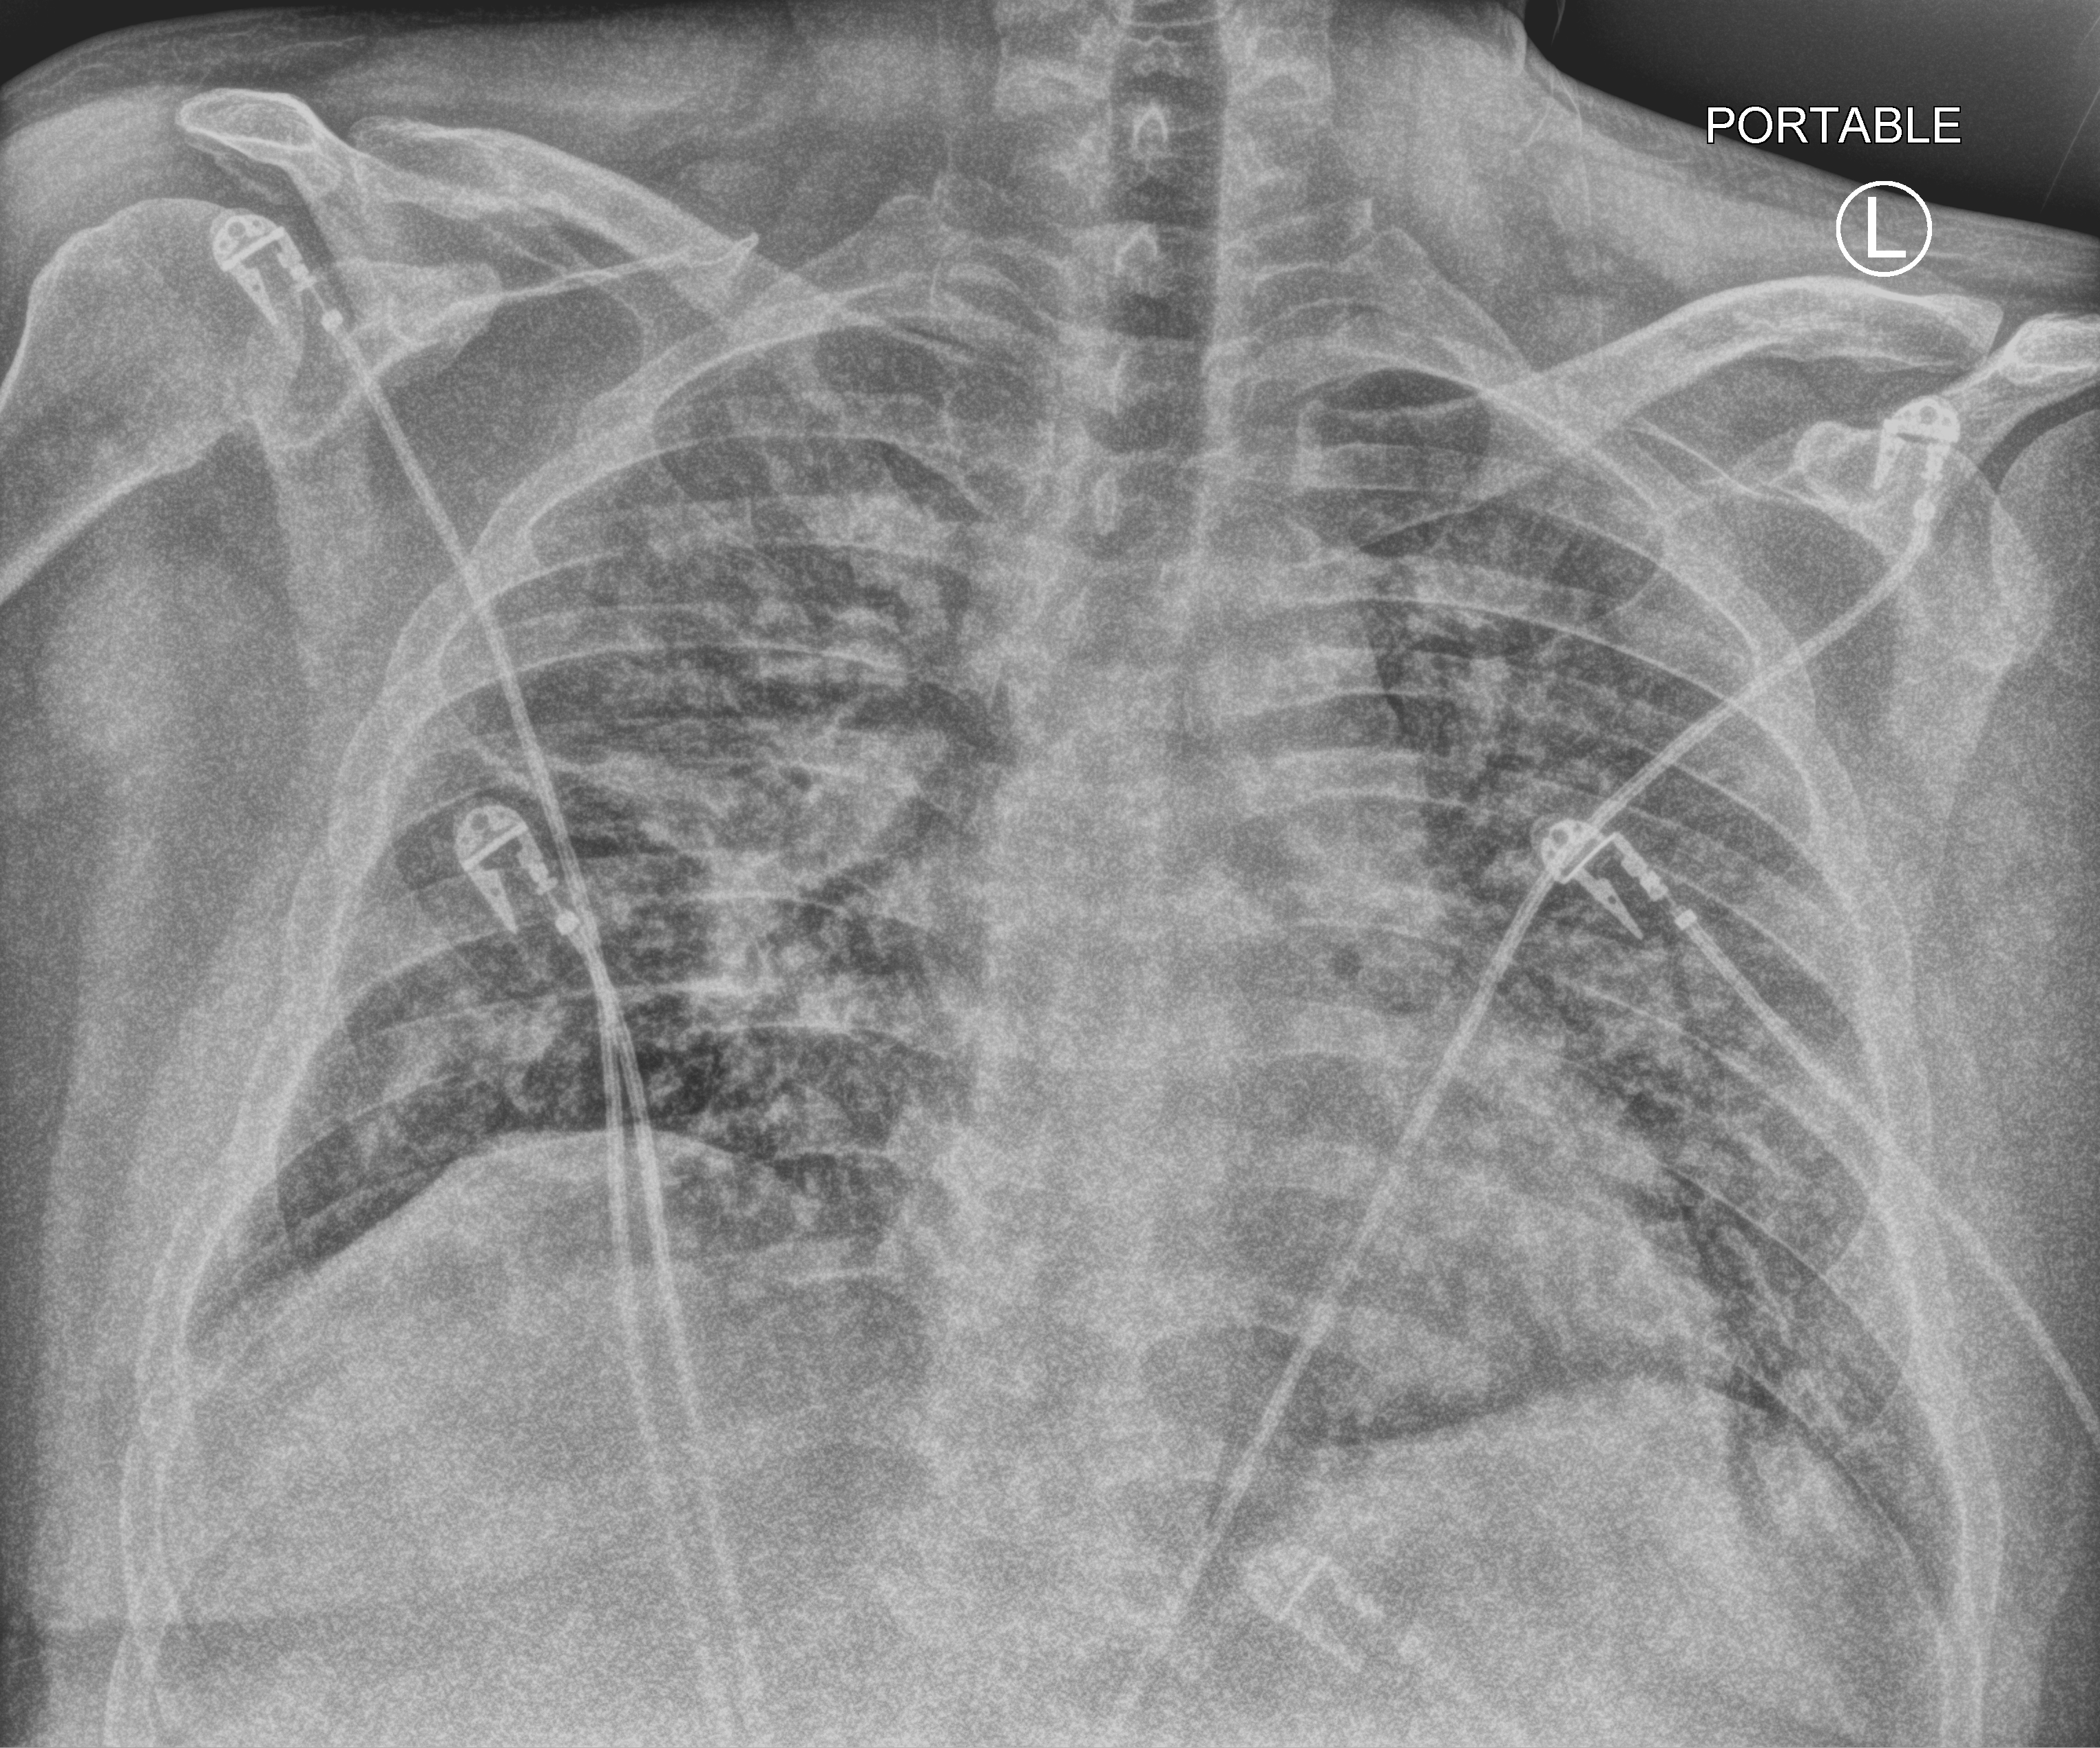
Chest X-ray (portable); anteroposterior (AP) projection. Patient hospitalised with COVID-19, aged 18–59 years.
From the hospital-stay record, not from the radiograph (when in the stay this image was taken is not recorded):
- mechanically ventilated during this hospital stay: yes
- length of hospital stay: 31 days
- admitted to intensive care during this hospital stay: yes